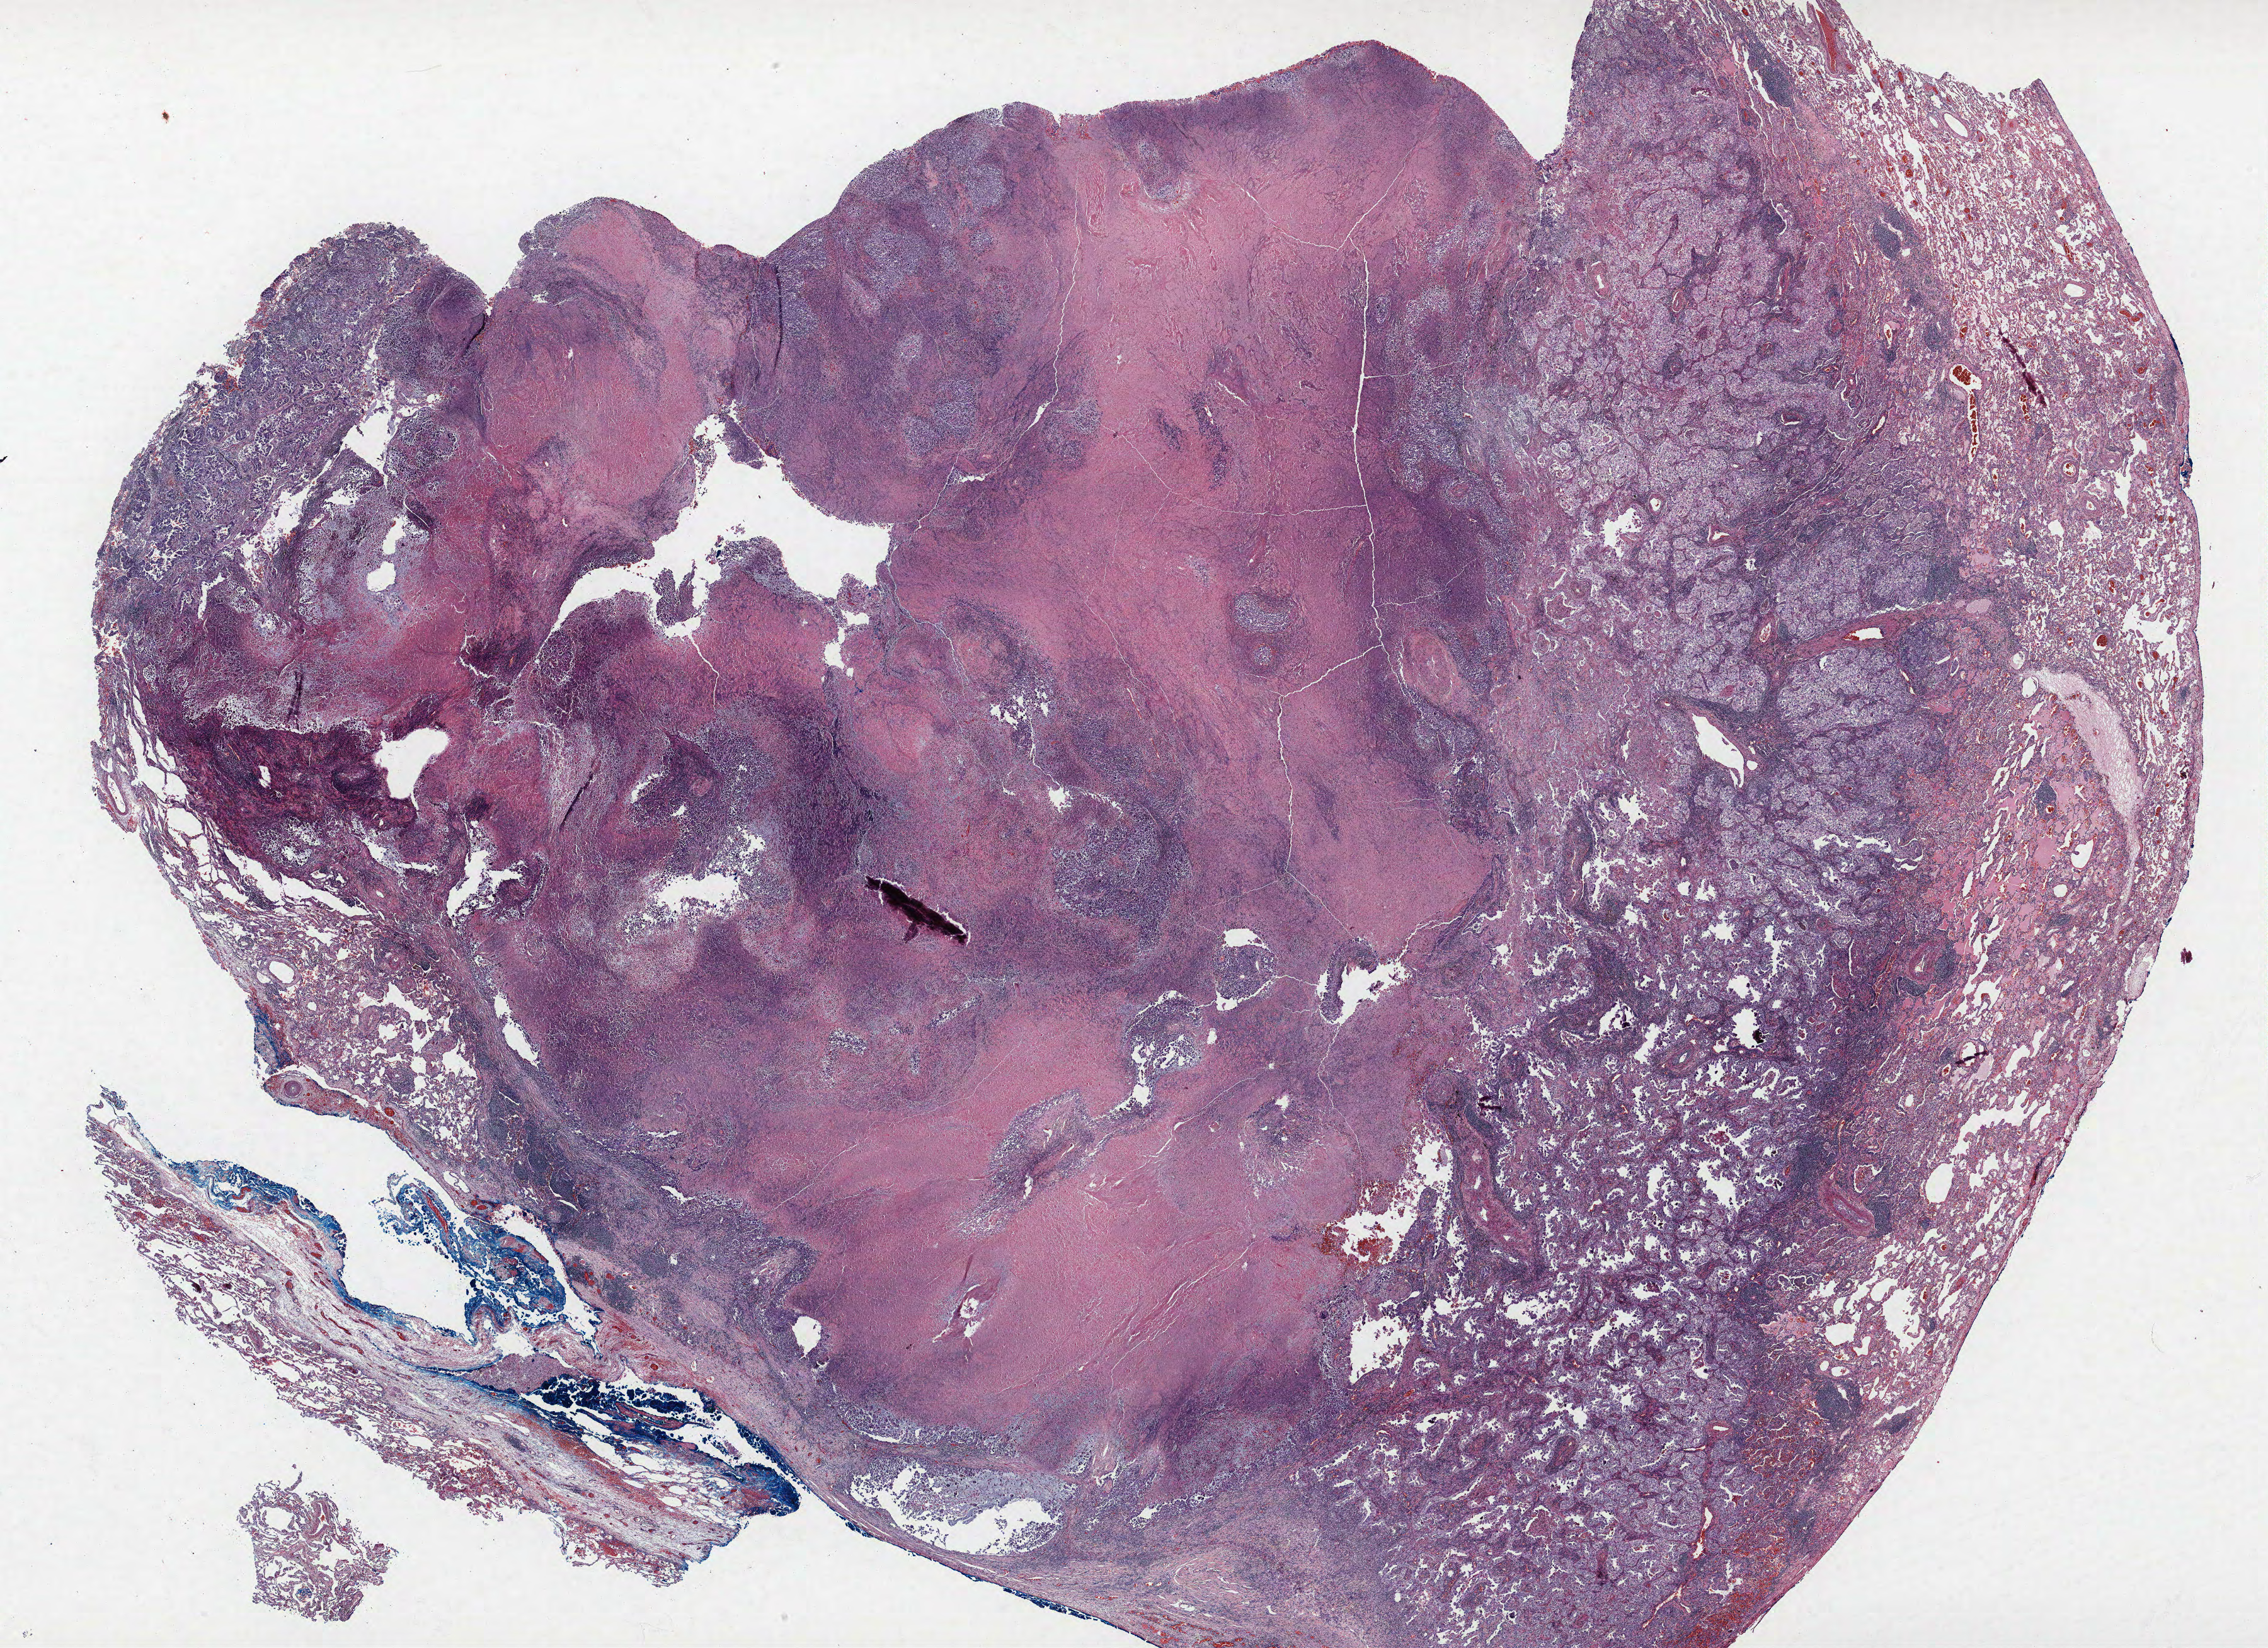
Whole-slide histology image, Hematoxylin and eosin (H&E) stained — shown as a low-resolution overview of the whole scanned area (about 28.8 x 20.9 mm, acquisition: 40x scan). FFPE section. Lung. Female, age 64 at enrolment. Current smoker at enrolment. Grade: poorly differentiated (G3).
* stage (AJCC 6th edition): IV
* participant's lung-cancer diagnosis: Adenocarcinoma, NOS (ICD-O-3 8140/3)
* primary tumour location (clinical record): left upper lobe, left lower lobe
* tumour size (pathology): 25 mm